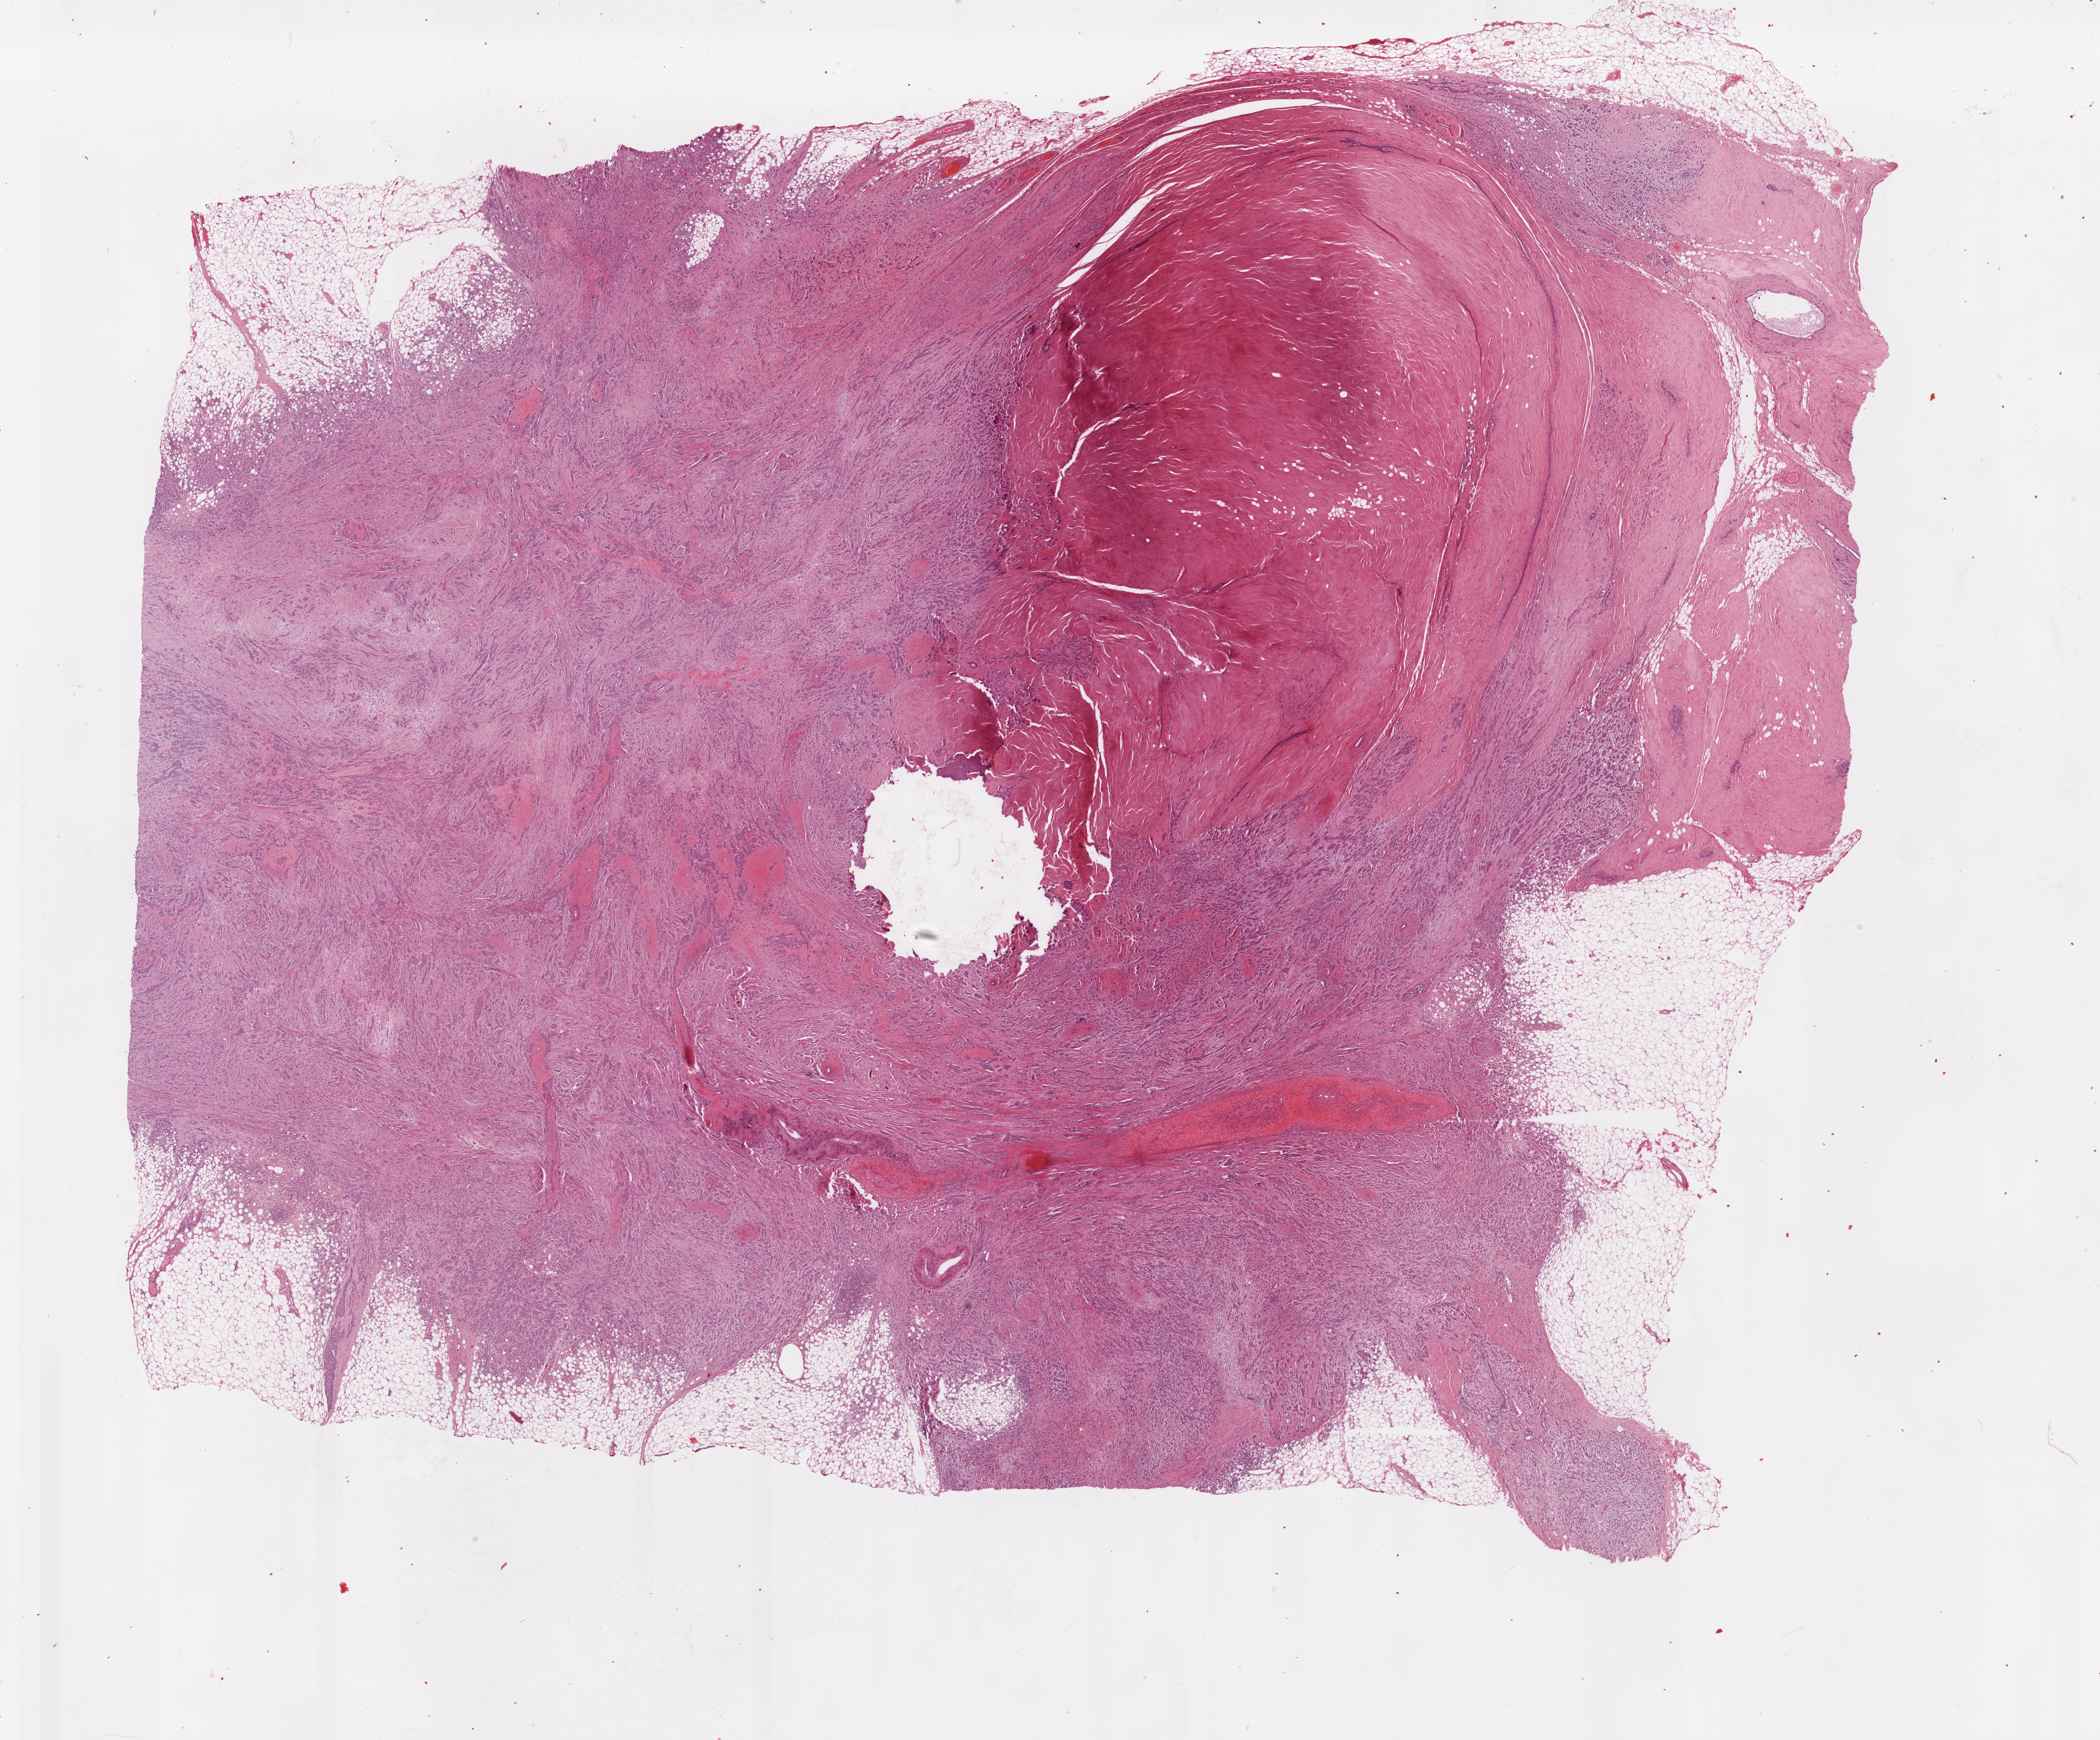
Whole-slide histology image, H&E-stained — low-resolution overview of the scanned area, about 24.9 x 20.6 mm (from a 40x scan); formalin-fixed paraffin-embedded (FFPE) diagnostic section; breast, primary tumour sample. Female, age 53 years at initial diagnosis.
Laterality: right. AJCC pathologic stage: IIIC (7th edition). Diagnosis: Lobular carcinoma, NOS.